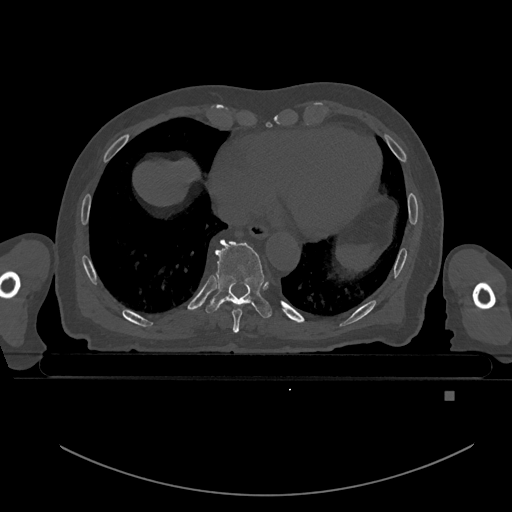
CT including the spine, one axial slice; position 161 of 969 along the scan axis; bone window (W 1800 / L 400 HU); 0.5 mm slice thickness; 512 × 512 image matrix, field of view 456 × 456 mm. Male patient, age 82 years. Case-level facts recorded for this patient, not image findings: primary cancer: prostate; vertebrae with lytic lesions (as recorded): T11, T9, T8, T2.
Annotated regions visible in this slice (semi-automatically segmented with operator editing):
- T8 vertebra: box from (x=232, y=298) to (x=243, y=333) px
- T9 vertebra: (x=206, y=239)–(x=272, y=318)